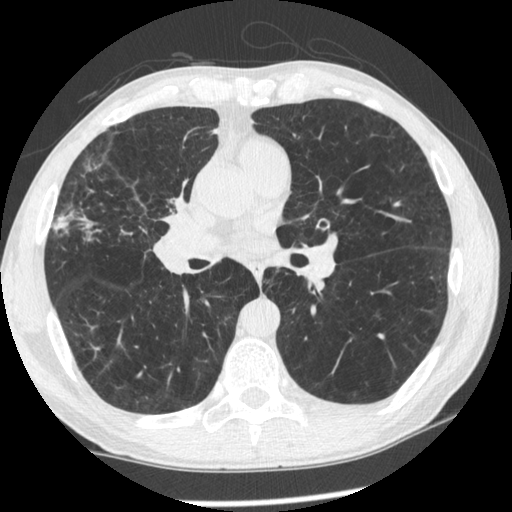
Low-dose screening chest CT, one axial slice; position 123 of 261 along the scan axis; reconstruction kernel STANDARD; 120 kVp; lung window (W 1500 / L -600 HU); 512 × 512 image matrix, field of view 340 × 340 mm.
Outlined on this slice (outlined manually by an expert reader):
- lesion 1 (tumor, upper lobe of right lung): box from (x=171, y=195) to (x=187, y=212) px